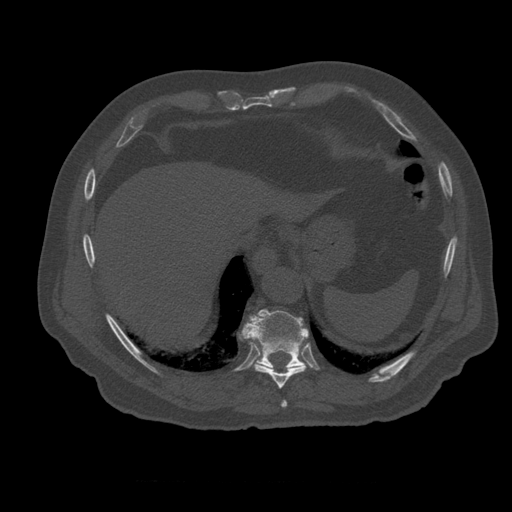
CT including the spine, one axial slice. Reconstruction kernel STANDARD. 120 kVp. Bone window (W 1800 / L 400 HU). 1.25 mm slice thickness. 512 × 512 image matrix, field of view 407 × 407 mm. Patient age 73 years. Case-level facts recorded for this patient, not image findings: primary cancer: prostate.
Annotated regions visible in this slice (semi-automatic segmentation, software-assisted and operator-edited):
- T10 vertebra: bounding box (x1, y1, x2, y2) in pixels: (240, 310, 309, 369)
- T12 vertebra: (267, 346, 280, 360)
- T8 vertebra: (281, 401, 288, 408)
- T9 vertebra: (254, 345, 307, 389)